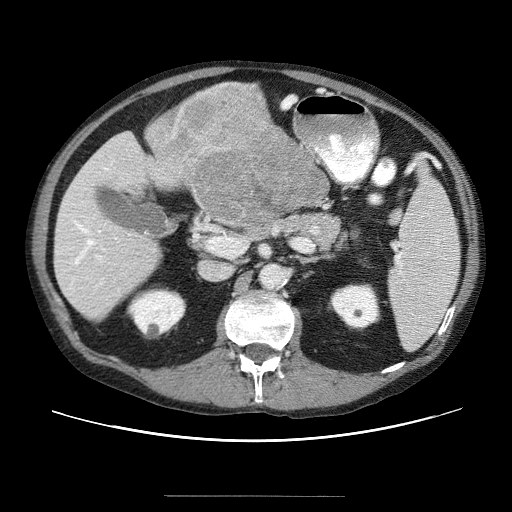
Contrast-enhanced abdominal CT (liver protocol), one axial slice; position 16 of 69 along the scan axis; reconstruction kernel STANDARD; 120 kVp; soft-tissue window (W 400 / L 40 HU); 2.5 mm slice thickness; 512 × 512 image matrix, field of view 380 × 380 mm. Case-level facts recorded for this patient, not image findings: diagnosis: hepatocellular carcinoma (patient treated with transarterial chemoembolisation; whether this scan precedes or follows treatment is not stated here); TNM stage (as recorded): Stage-IVB; Child-Pugh class: B; tumour differentiation: poorly differentiated.
Structures marked on this image (semi-automatically segmented with operator editing):
- liver parenchyma outside the tumour (the mass and vessels are separate outlines, so this box may not span the whole liver): bounding box <54,136,203,314> (left, top, right, bottom; pixels)
- mass: <147,85,329,227>
- liver vessels: <60,149,130,298>